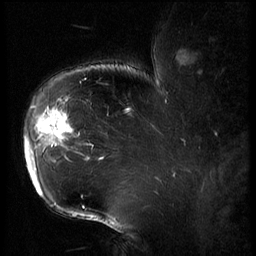
Breast MRI (dynamic contrast-enhanced), one sagittal slice; slice 47 of 62 in the series (ordered by position); 3 images stored at this slice position (order not interpretable as contrast timing); 1.5 T; TE 4.2 ms, TR 9 ms; 256 × 256 image matrix. Female patient, age 43 years. From the clinical record (not read from this slice): setting: breast cancer imaged before/during neoadjuvant chemotherapy; receptor status: HER2-positive.
Annotated regions visible in this slice (semi-automatic segmentation, software-assisted and operator-edited):
- analysis volume of interest (the breast-tissue region the enhancement analysis was run in; not a lesion): bounding box [x1, y1, x2, y2] px = [23, 90, 82, 203]
- tumour enhancement mask (voxels above the 140 % enhancement threshold inside the analysis volume of interest): [26, 100, 76, 194]